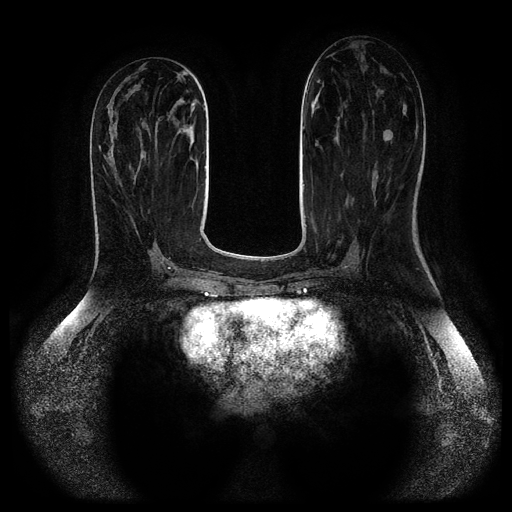
Breast MRI (dynamic contrast-enhanced, multi-phase), one axial slice; position 40 of 116 along the scan axis; dynamic contrast-enhanced series, time point 2 of 5 at this slice position (early post-contrast); 1.5 T; TE 2.6 ms, TR 5.2 ms; 2 mm slice thickness; 512 × 512 image matrix, field of view 380 × 380 mm. Patient: female, 44 years.
Outlined on this slice (semi-automatic segmentation, software-assisted and operator-edited):
- breast lesion (labelled benign in the annotation): box from (x=384, y=130) to (x=391, y=142) px